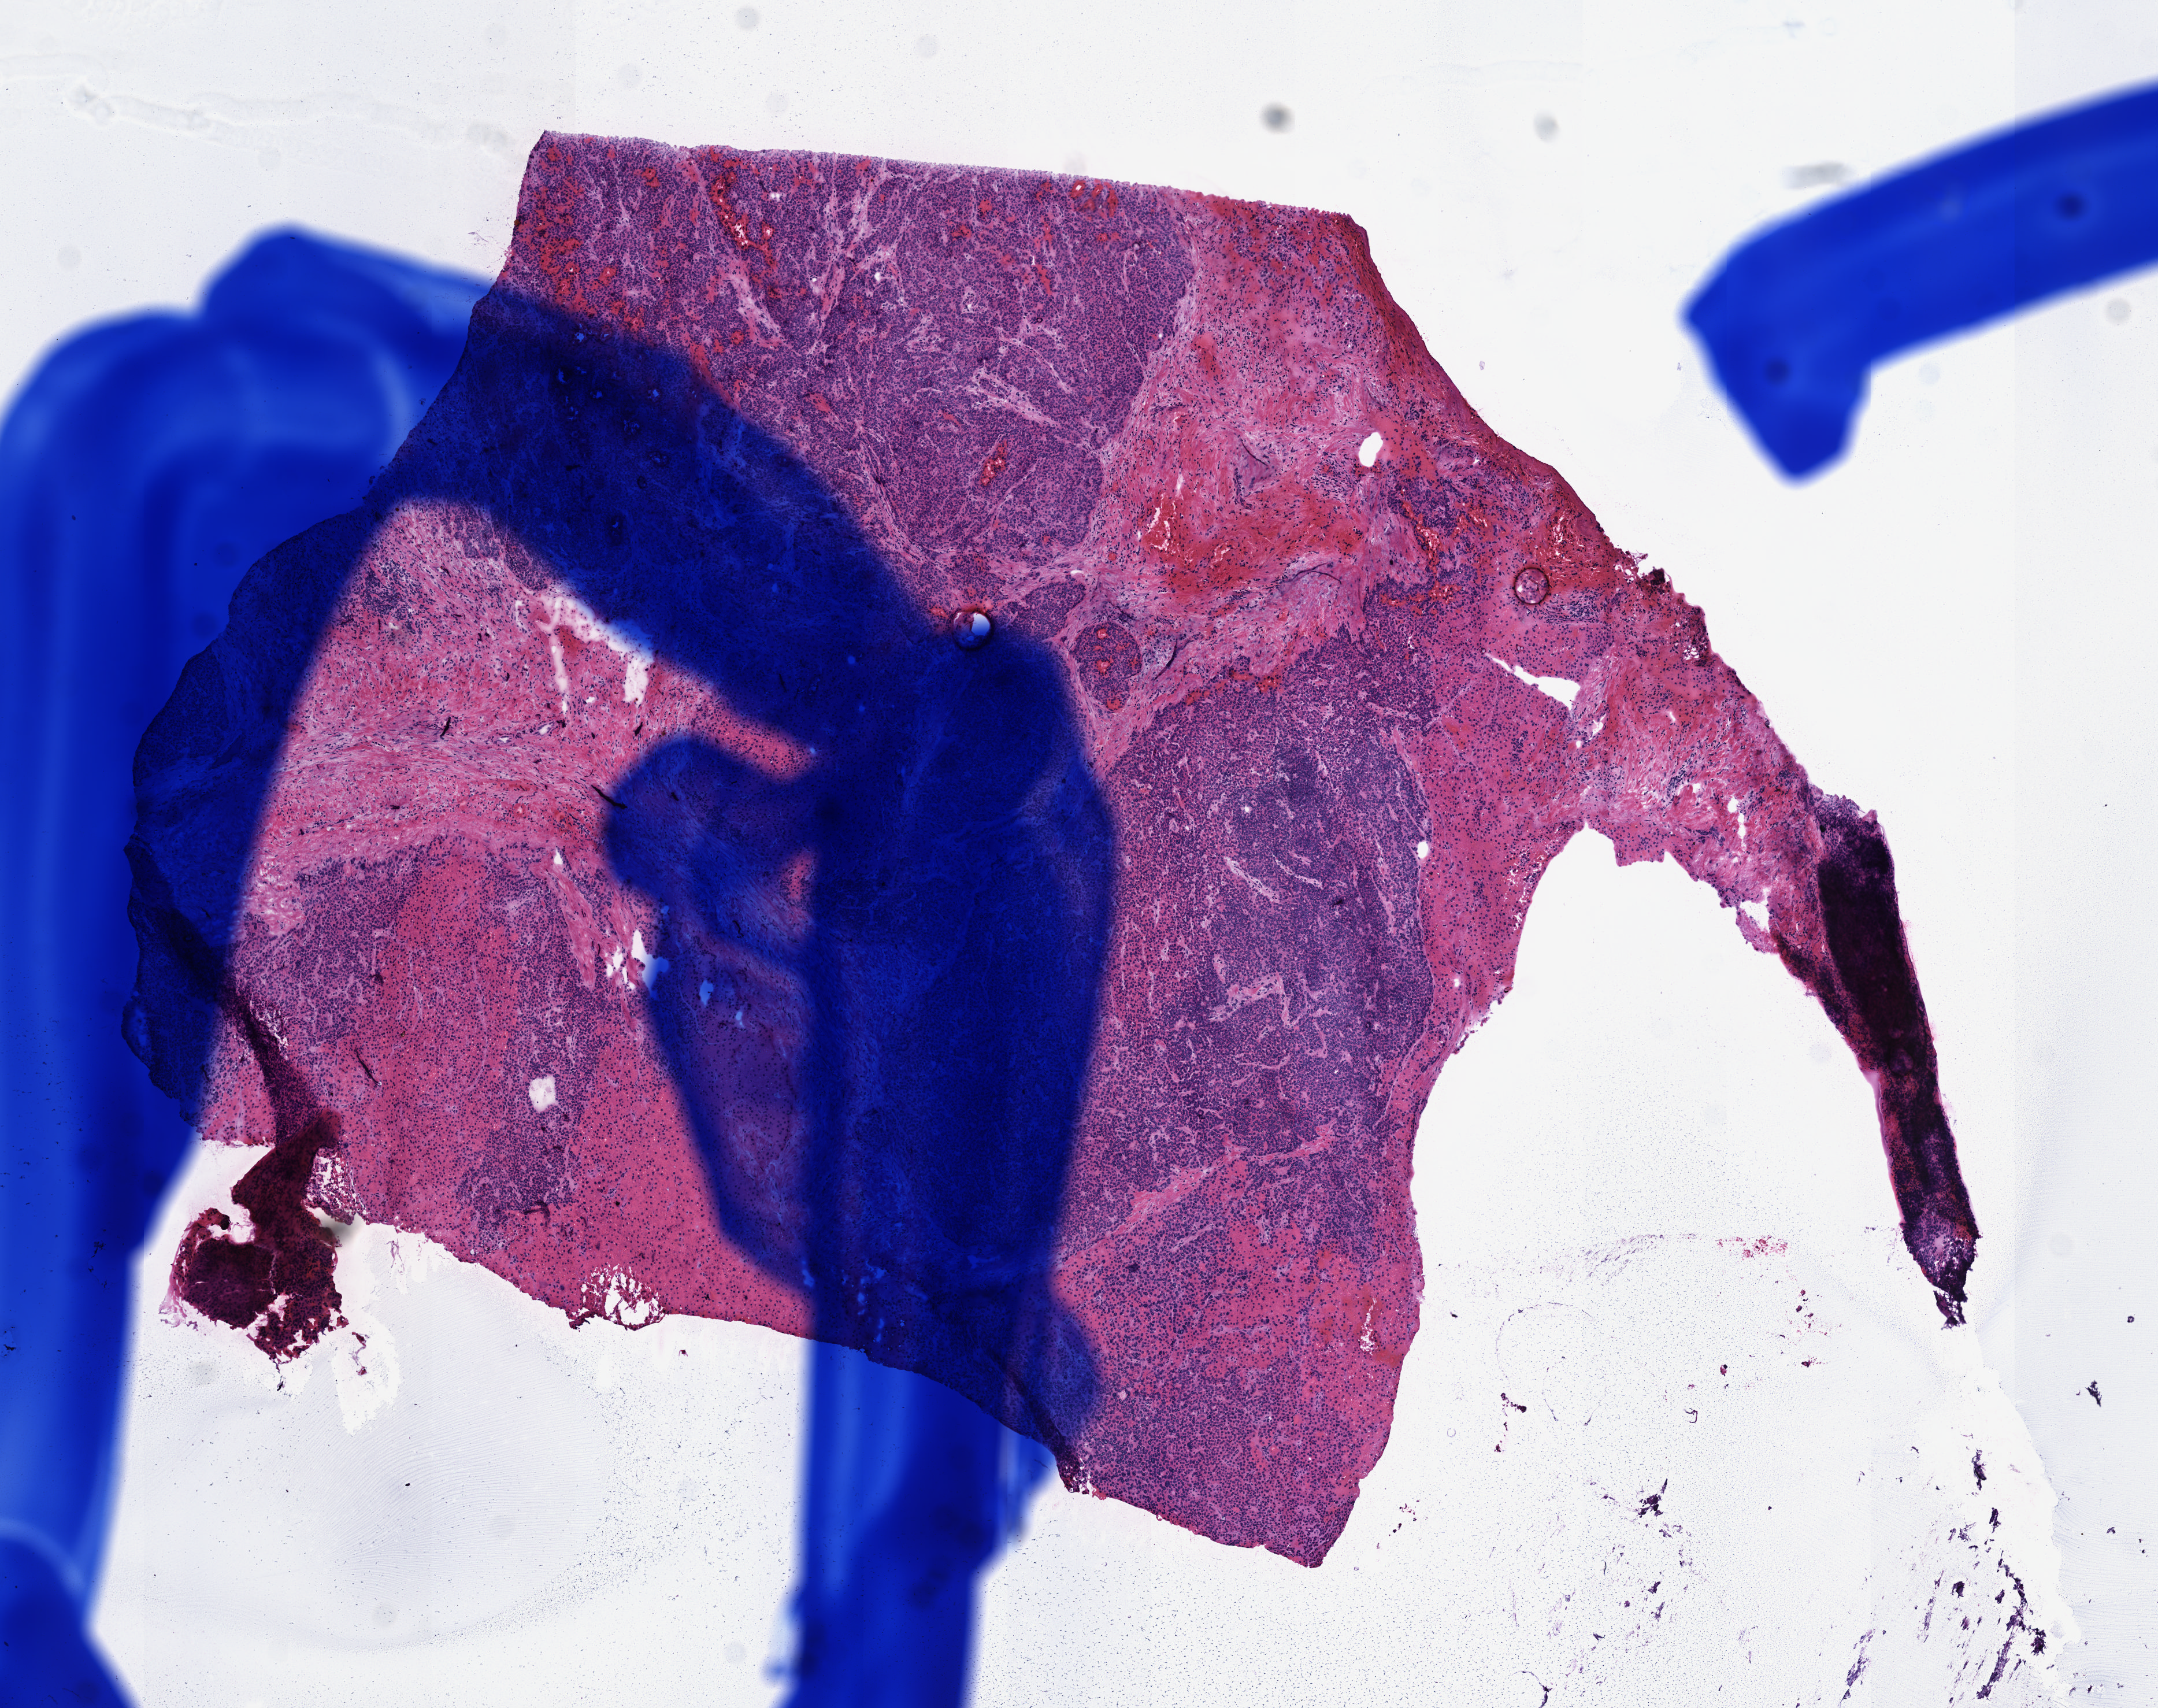
Digitized Hematoxylin and eosin (H&E) stained tissue section (whole slide) — shown as a low-resolution overview of the whole scanned area (about 7.6 x 6.0 mm, from a 40x scan); frozen section from the top of the tissue portion; liver, primary tumour sample. Male patient; age at initial diagnosis 58 years. Pathologist review of this section (percent, as recorded): tumour cells 70%, tumour nuclei 70%.
Pathologic diagnosis: Hepatocellular carcinoma, NOS.